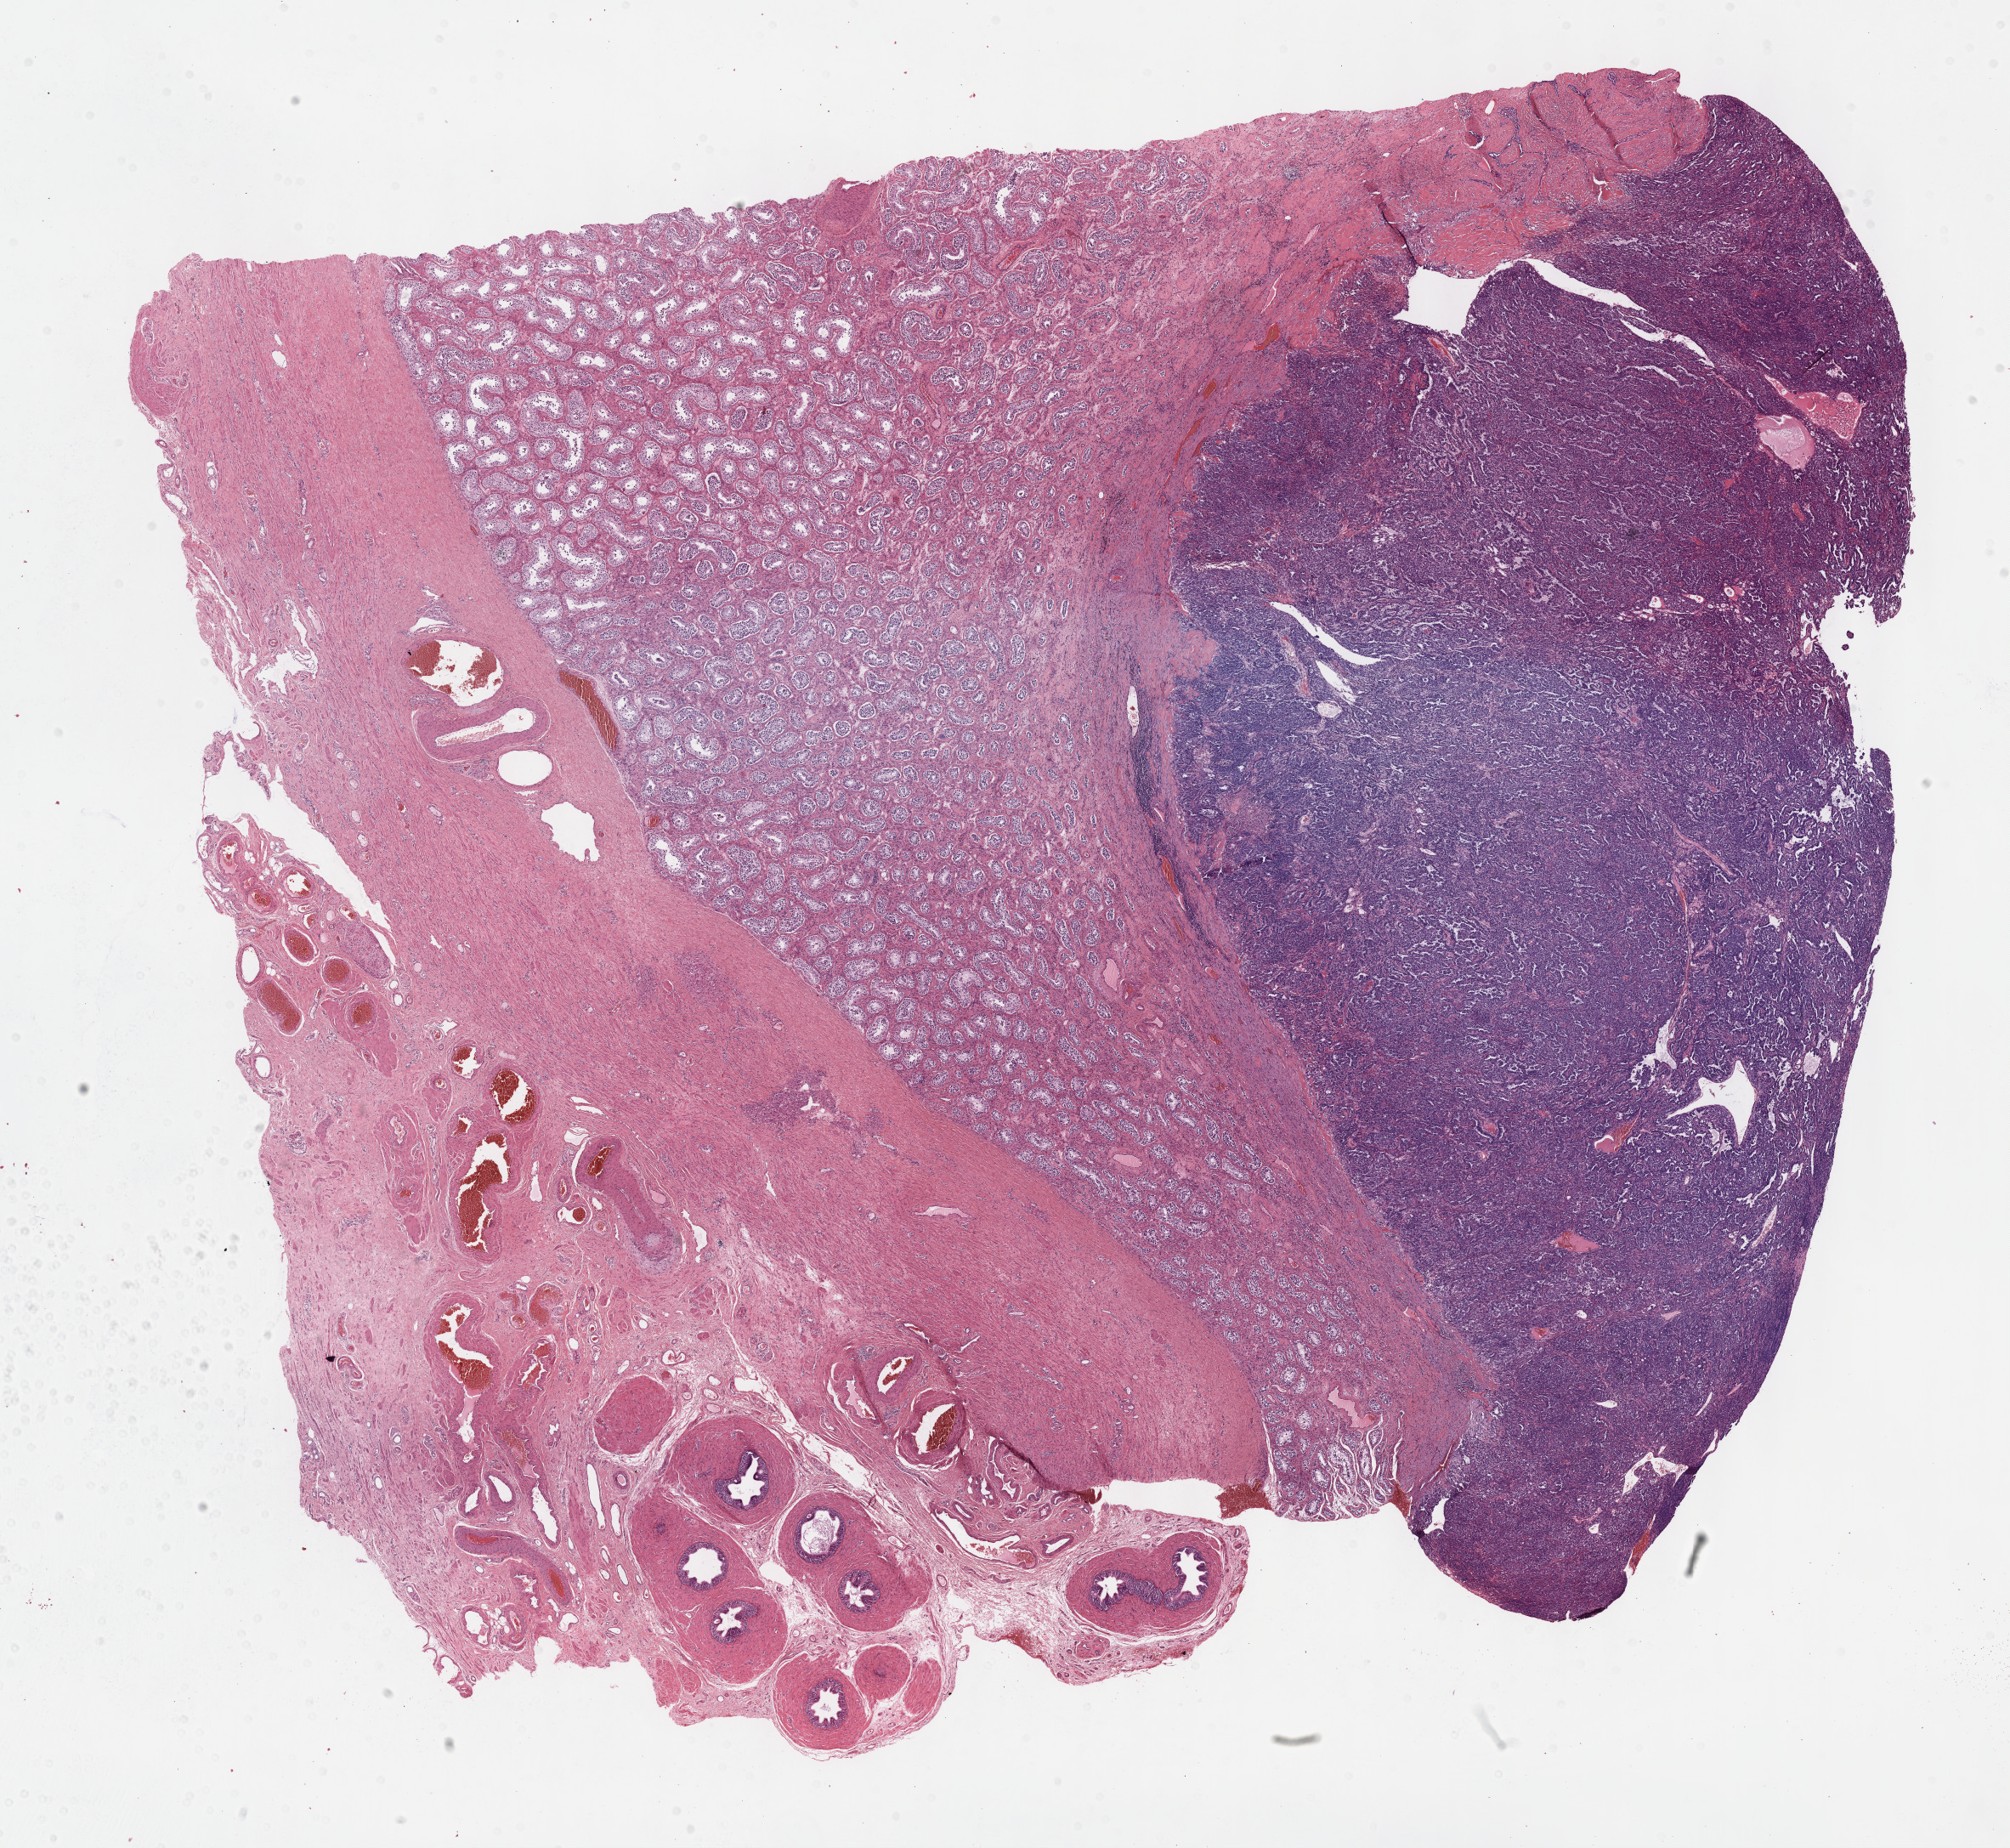
Hematoxylin and eosin (H&E) stained whole-slide image, a low-resolution overview of the entire scanned area, about 19.1 x 17.6 mm (from a 40x scan), FFPE section, testis, primary tumour sample. Patient: male, age at initial diagnosis 27 years.
AJCC pathologic stage: IIIC. Histologic diagnosis: Embryonal carcinoma, NOS.